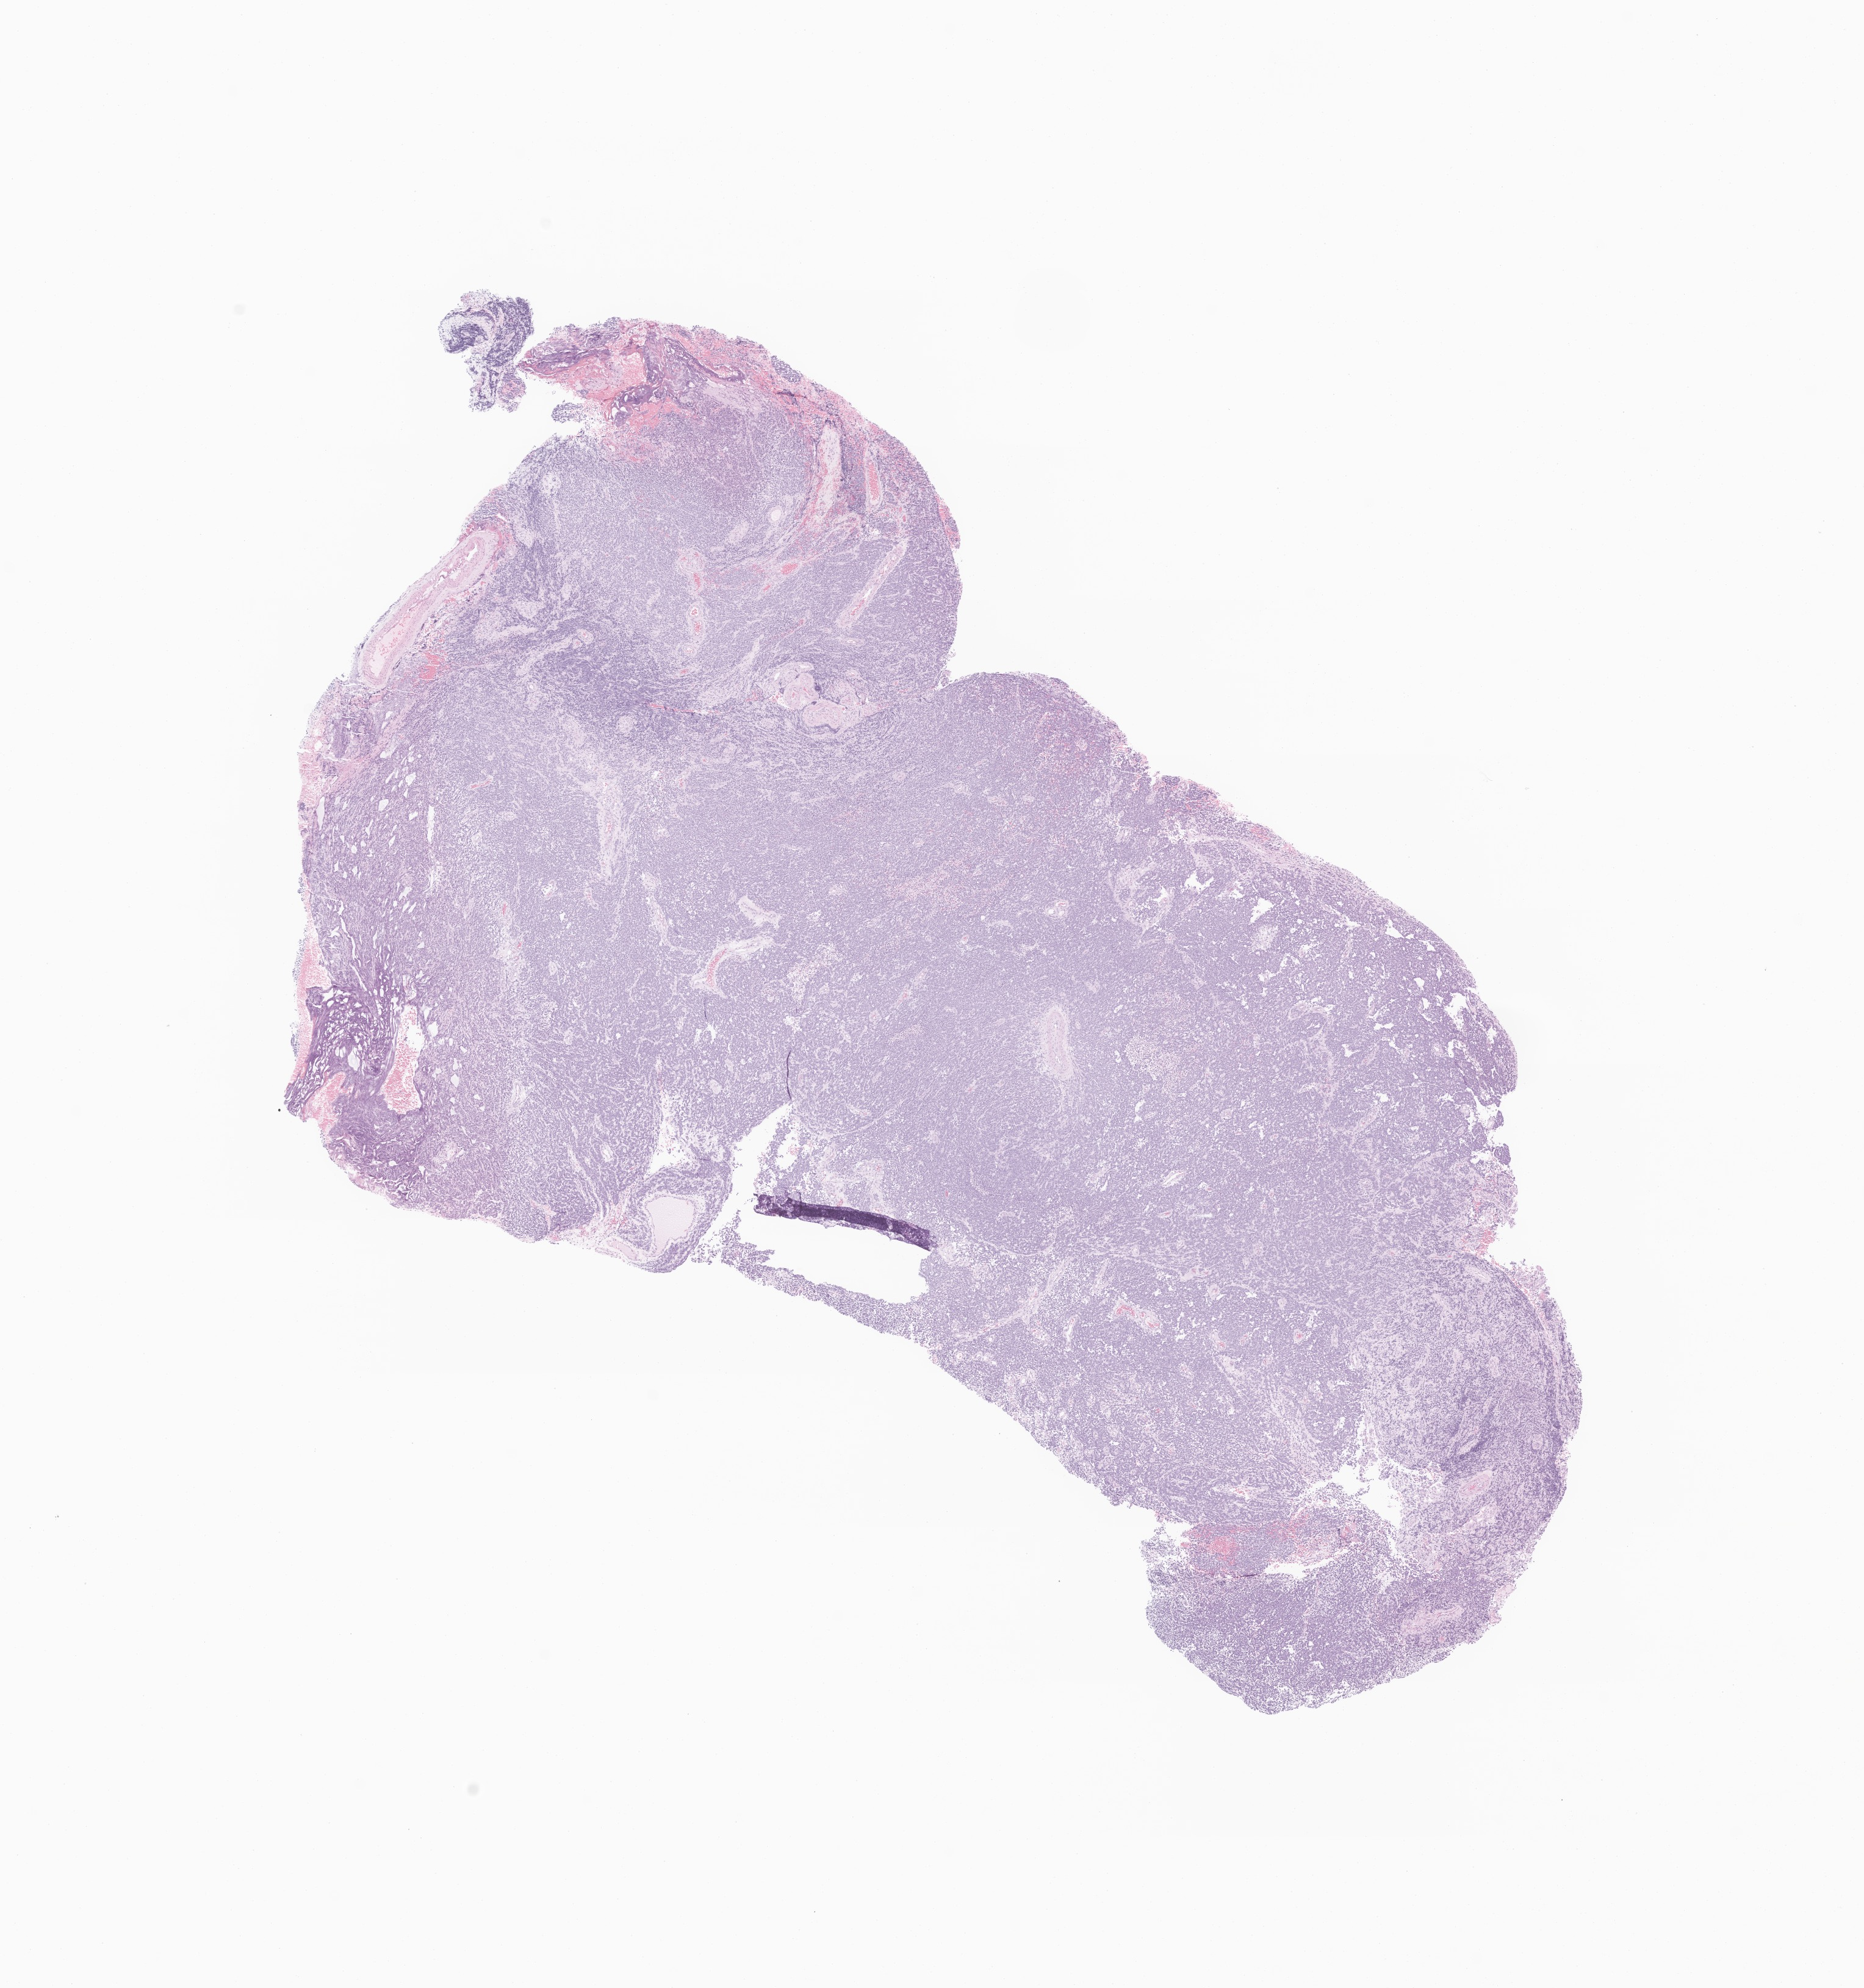
Haematoxylin and eosin whole-slide image of tumor tissue from the cerebellum, low-resolution overview of the scanned area, about 12.9 x 13.7 mm. FFPE section. Patient: female, age 161 months (13 years 5 months).
• recorded diagnosis: Medulloblastoma, NOS